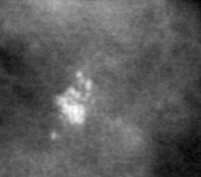
Region of interest cut from a scanned film mammogram (one marked finding); right breast; MLO view; BI-RADS breast density category 4 (scale 1–4).
- Marked abnormality: calcifications, morphology pleomorphic, distribution clustered; BI-RADS assessment category 4; subtlety rating 3 on a 1 (subtle) to 5 (obvious) scale; pathology (as recorded): benign.